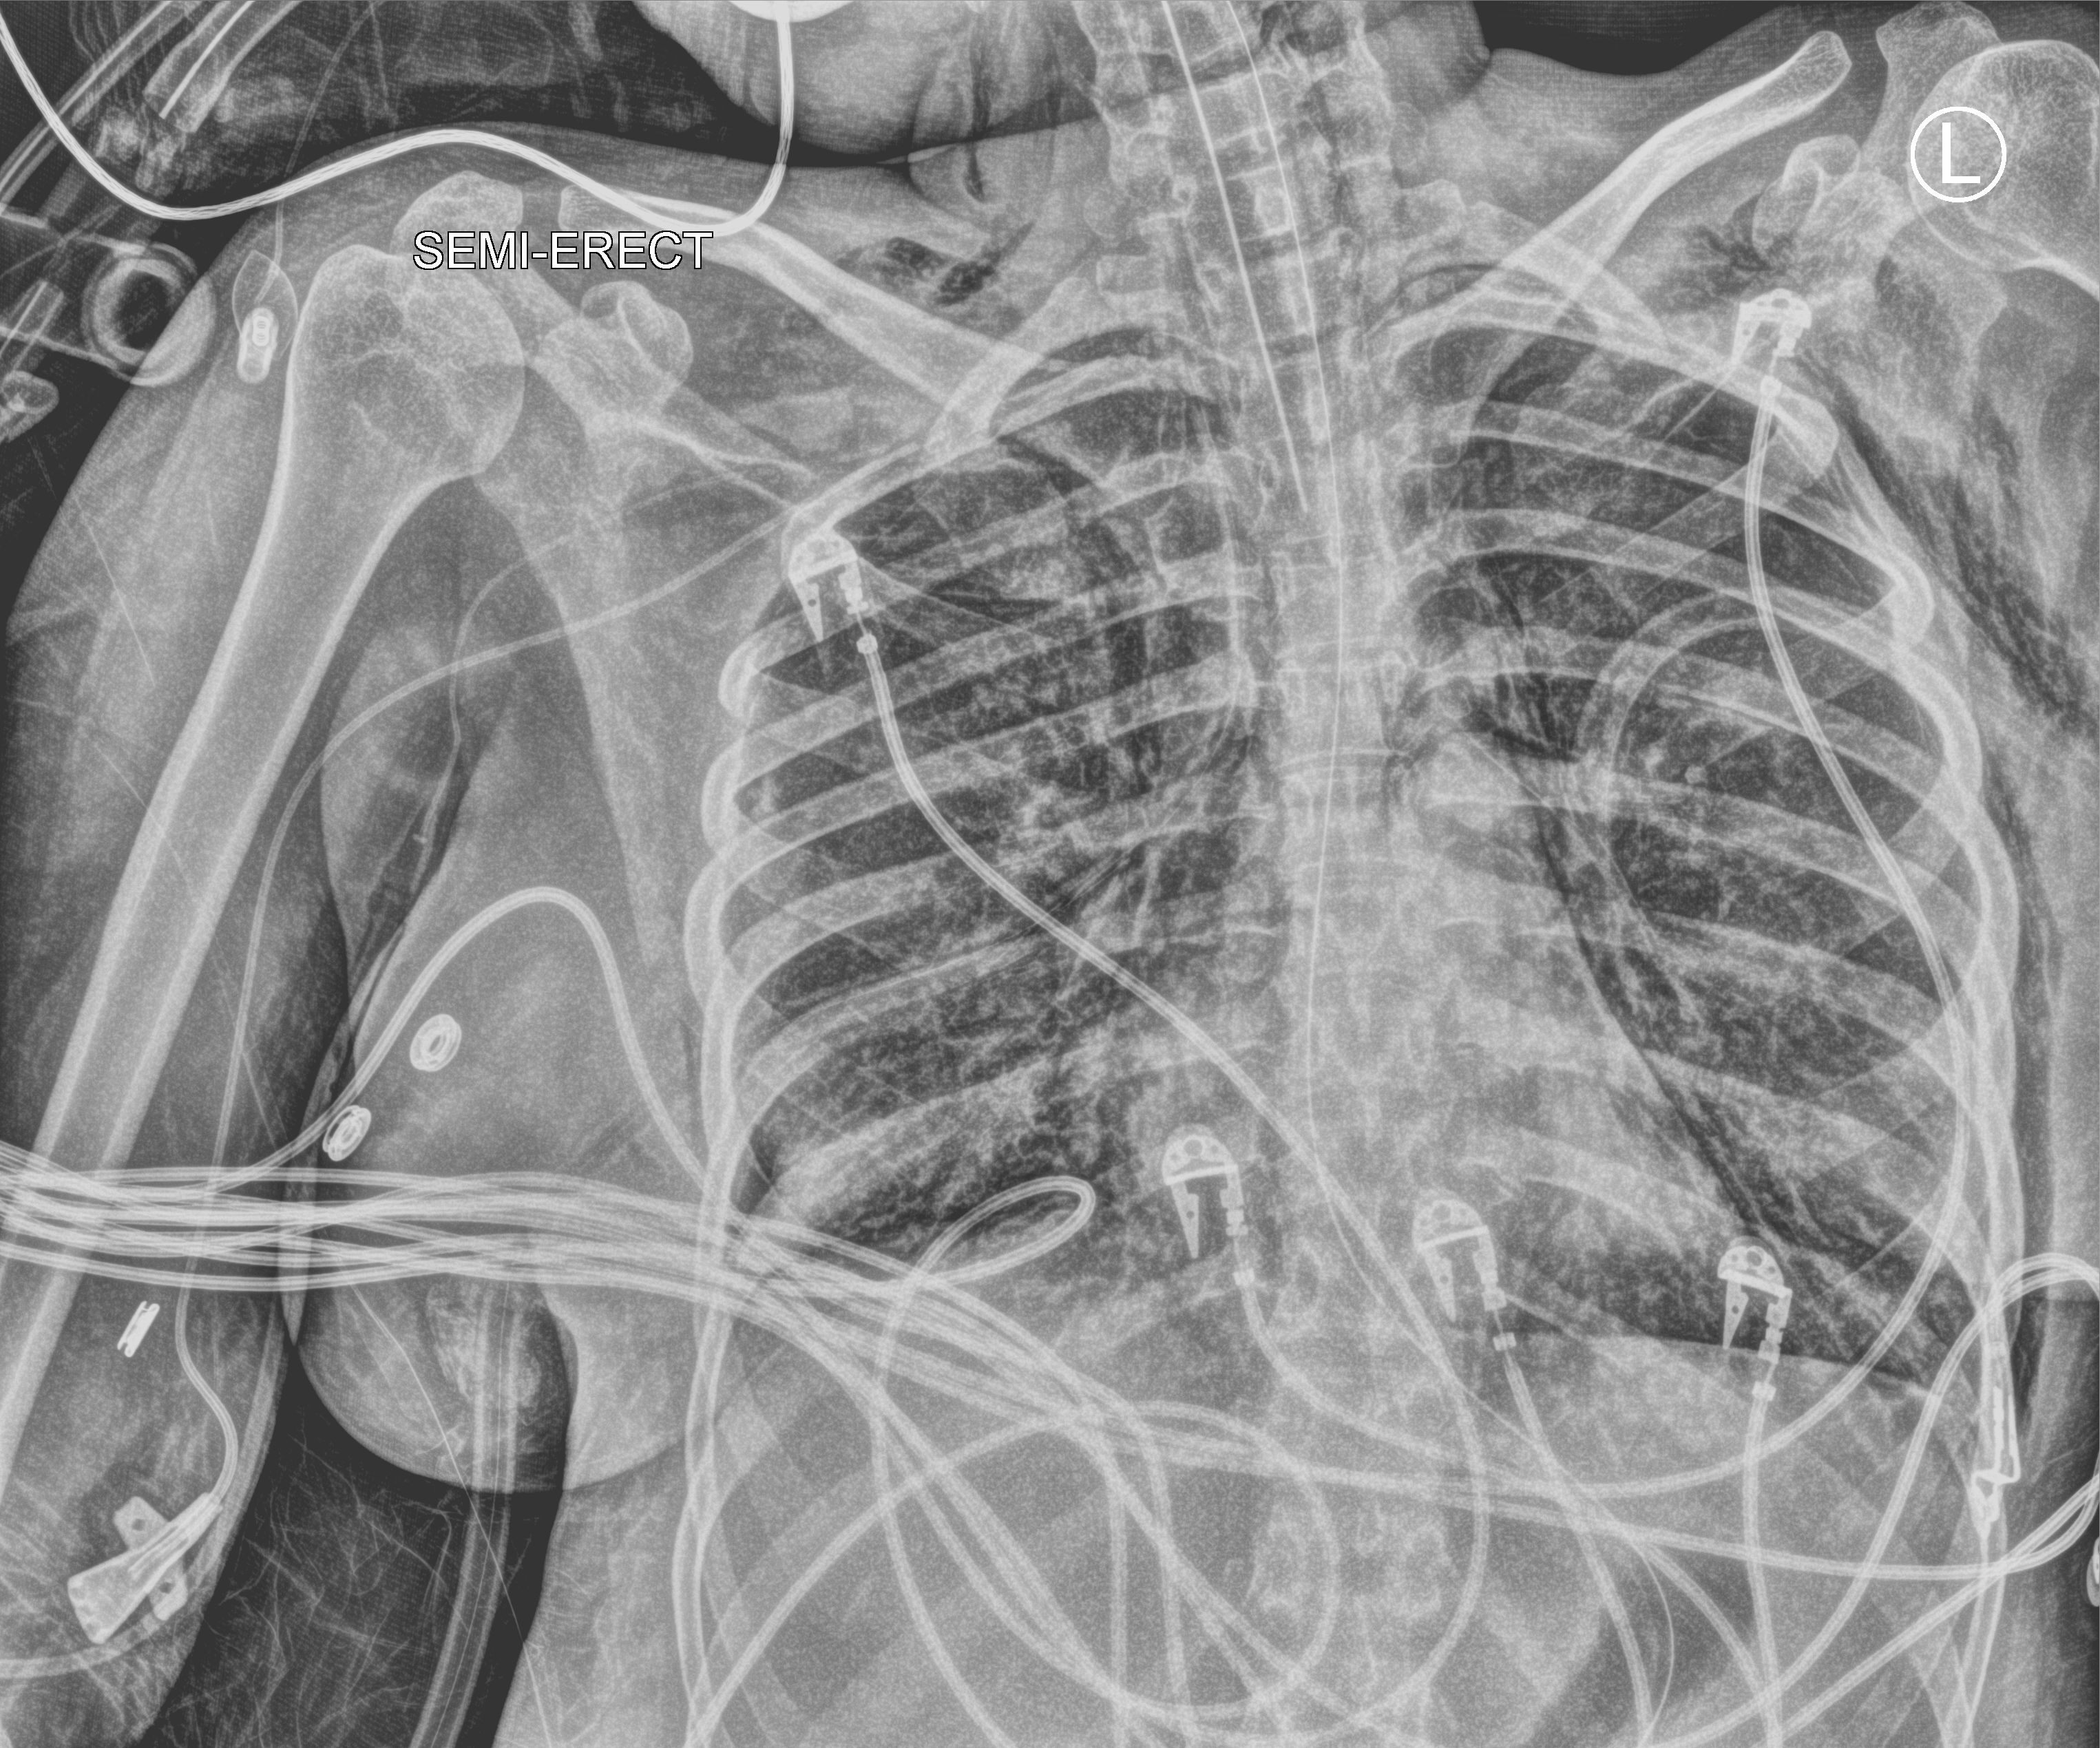
Chest X-ray (portable), anteroposterior (AP) projection. Patient hospitalised with COVID-19, aged 18–59 years.
From the hospital-stay record, not from the radiograph (when in the stay this image was taken is not recorded):
- other chronic lung disease (admission record): no
- mechanically ventilated during this hospital stay: yes